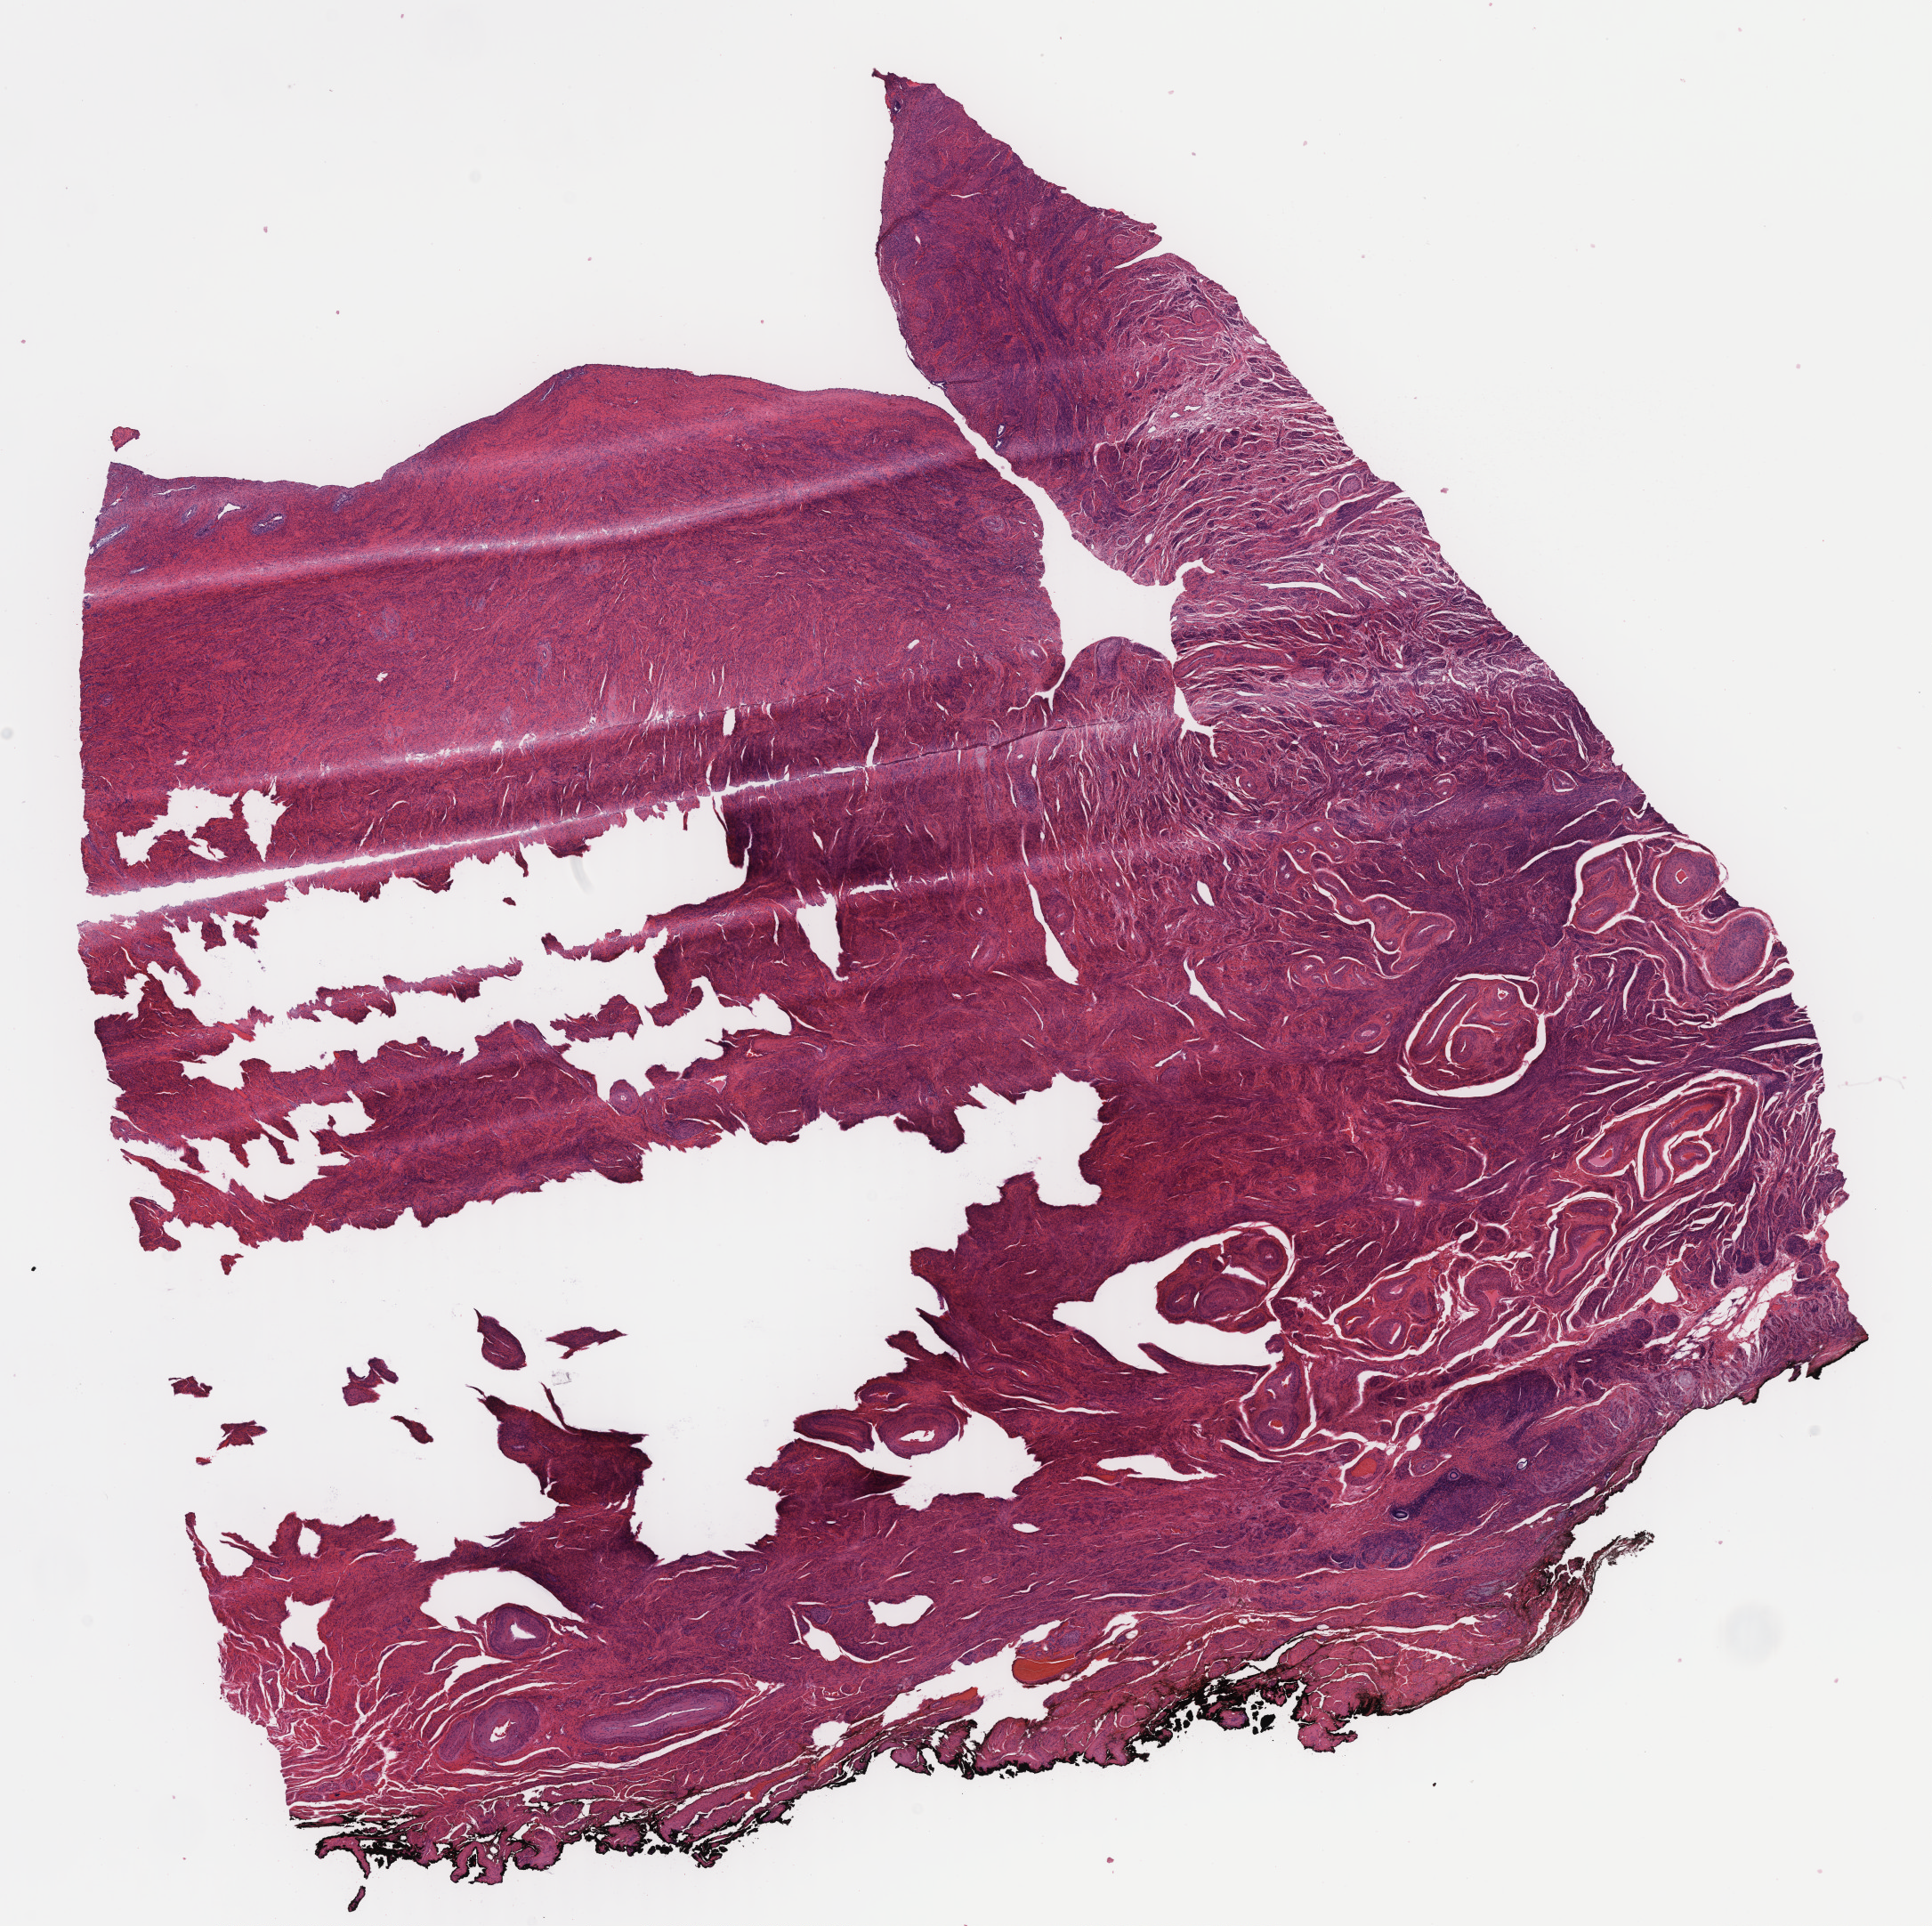
H&E whole-slide image, shown as a low-resolution overview of the whole scanned area (about 17.2 x 17.1 mm); frozen section (tissue freezing medium); non-tumor (normal tissue) sample from a patient with serous carcinoma, NOS; anatomic site: uterine fundus. Patient sex: female. Slide review estimates, as recorded: tumor cells 0%, tumor nuclei 0%, stromal cells 99%, necrosis 0%, normal cells 1%. Inflammatory infiltration, as recorded: lymphocyte infiltration 1%, monocyte infiltration 1%, neutrophil infiltration 0%.
This section: non-tumor tissue sample; the patient's diagnosis is given above.